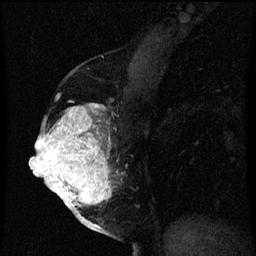
Breast MRI (dynamic contrast-enhanced), one sagittal slice. Position 29 of 60 along the scan axis. Dynamic contrast-enhanced series, image 2 of 3 at this slice position (ordered by acquisition). 1.5 T. TE 4.2 ms, TR 8 ms. 2 mm slice thickness. 256 × 256 image matrix, field of view 180 × 180 mm. Patient: female, 56 years.
Structures marked on this image (semi-automatically segmented with operator editing):
- analysis volume of interest (the breast-tissue region the enhancement analysis was run in; not a lesion): bounding box [x1, y1, x2, y2] px = [40, 104, 121, 219]
- tumour enhancement mask (voxels above the 70 % enhancement threshold inside the analysis volume of interest): [40, 104, 113, 219]